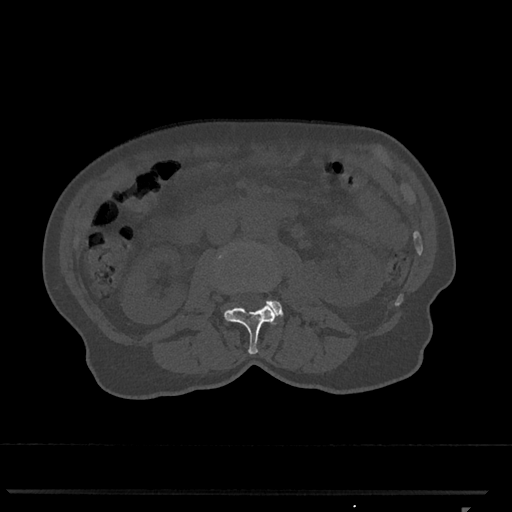
CT including the spine, one axial slice. Slice 314 of 793 in the series (ordered by position). 120 kVp. Bone window (W 1800 / L 400 HU). 0.5 mm slice thickness. 512 × 512 image matrix, field of view 380 × 380 mm. Female patient, age 62 years. Case-level facts recorded for this patient, not image findings: primary cancer: renal.
Structures marked on this image (semi-automatic segmentation, software-assisted and operator-edited):
- L2 vertebra: bounding box [x1, y1, x2, y2] px = [219, 252, 278, 354]
- L3 vertebra: [267, 301, 283, 317]